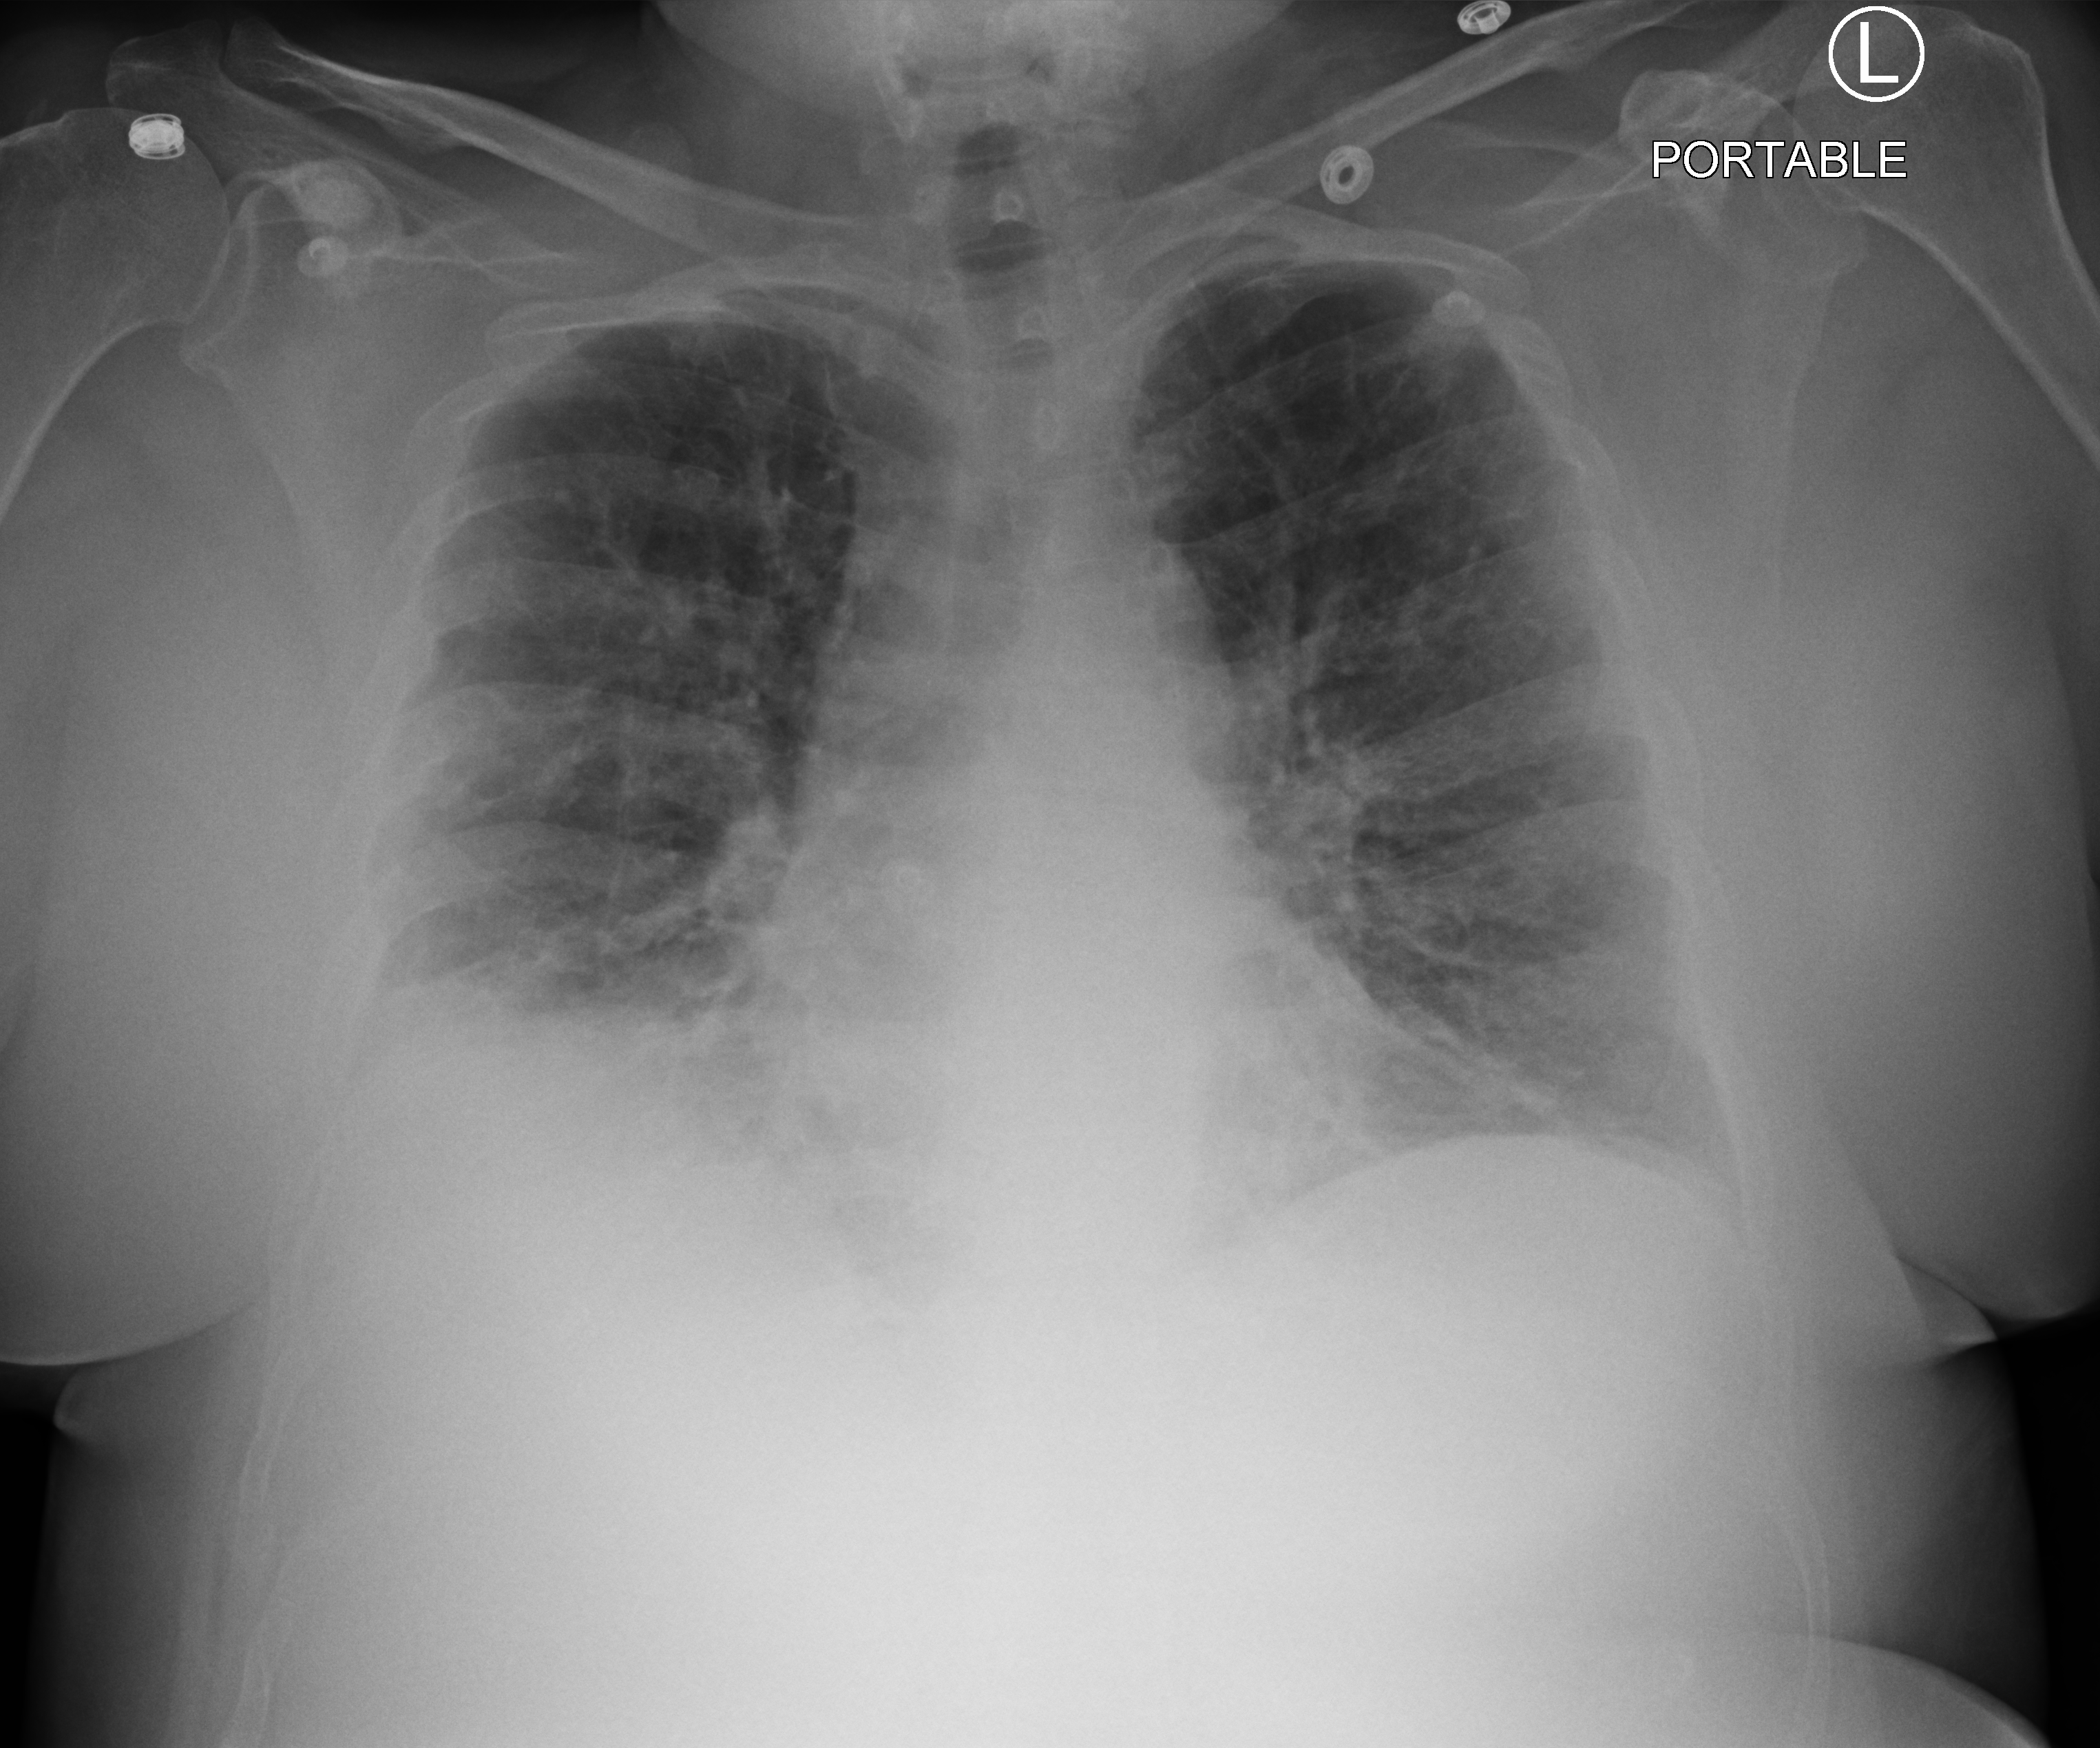
Chest X-ray (portable), anteroposterior (AP) projection. Female patient hospitalised with COVID-19, age 18–59 years.
Hospital-stay facts (about this admission, not read from this image; timing relative to this image not recorded): mechanically ventilated during this hospital stay: no; diabetes (admission record): no.